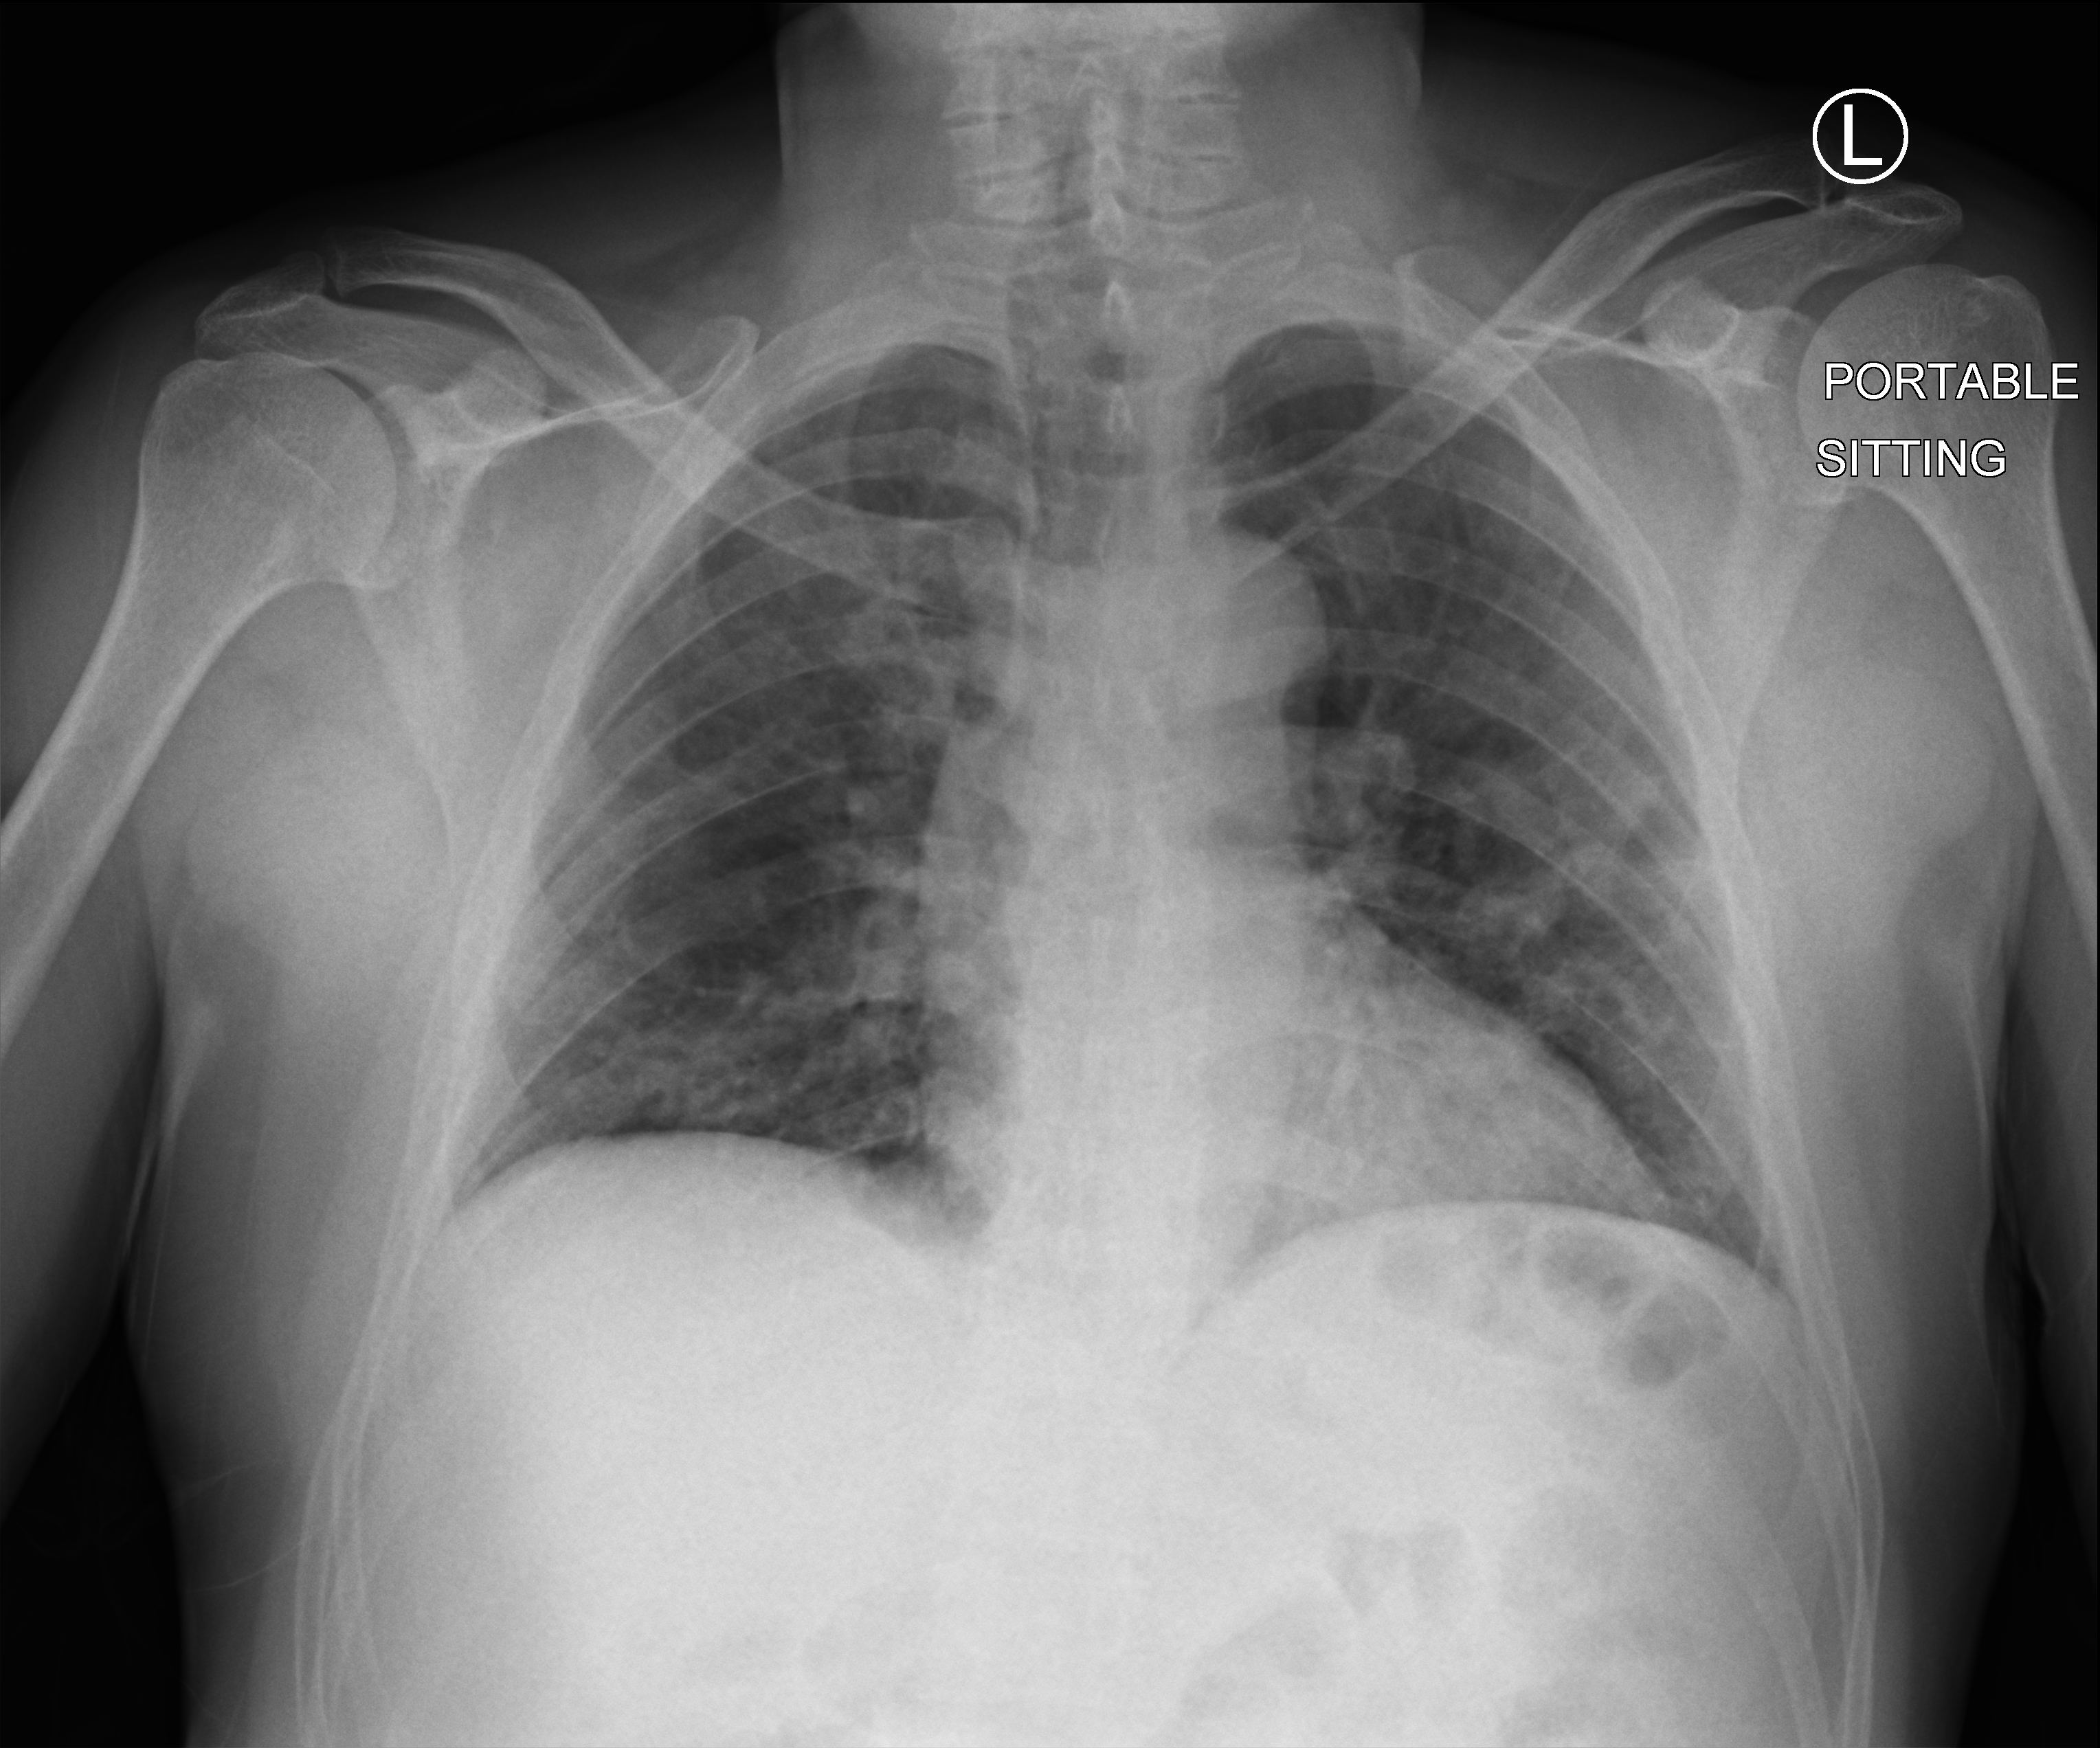
Chest X-ray (portable), anteroposterior (AP) projection. Patient hospitalised with COVID-19; male, aged 18–59 years.
From the hospital-stay record, not from the radiograph (when in the stay this image was taken is not recorded):
- mechanically ventilated during this hospital stay: no
- length of hospital stay: 3 days